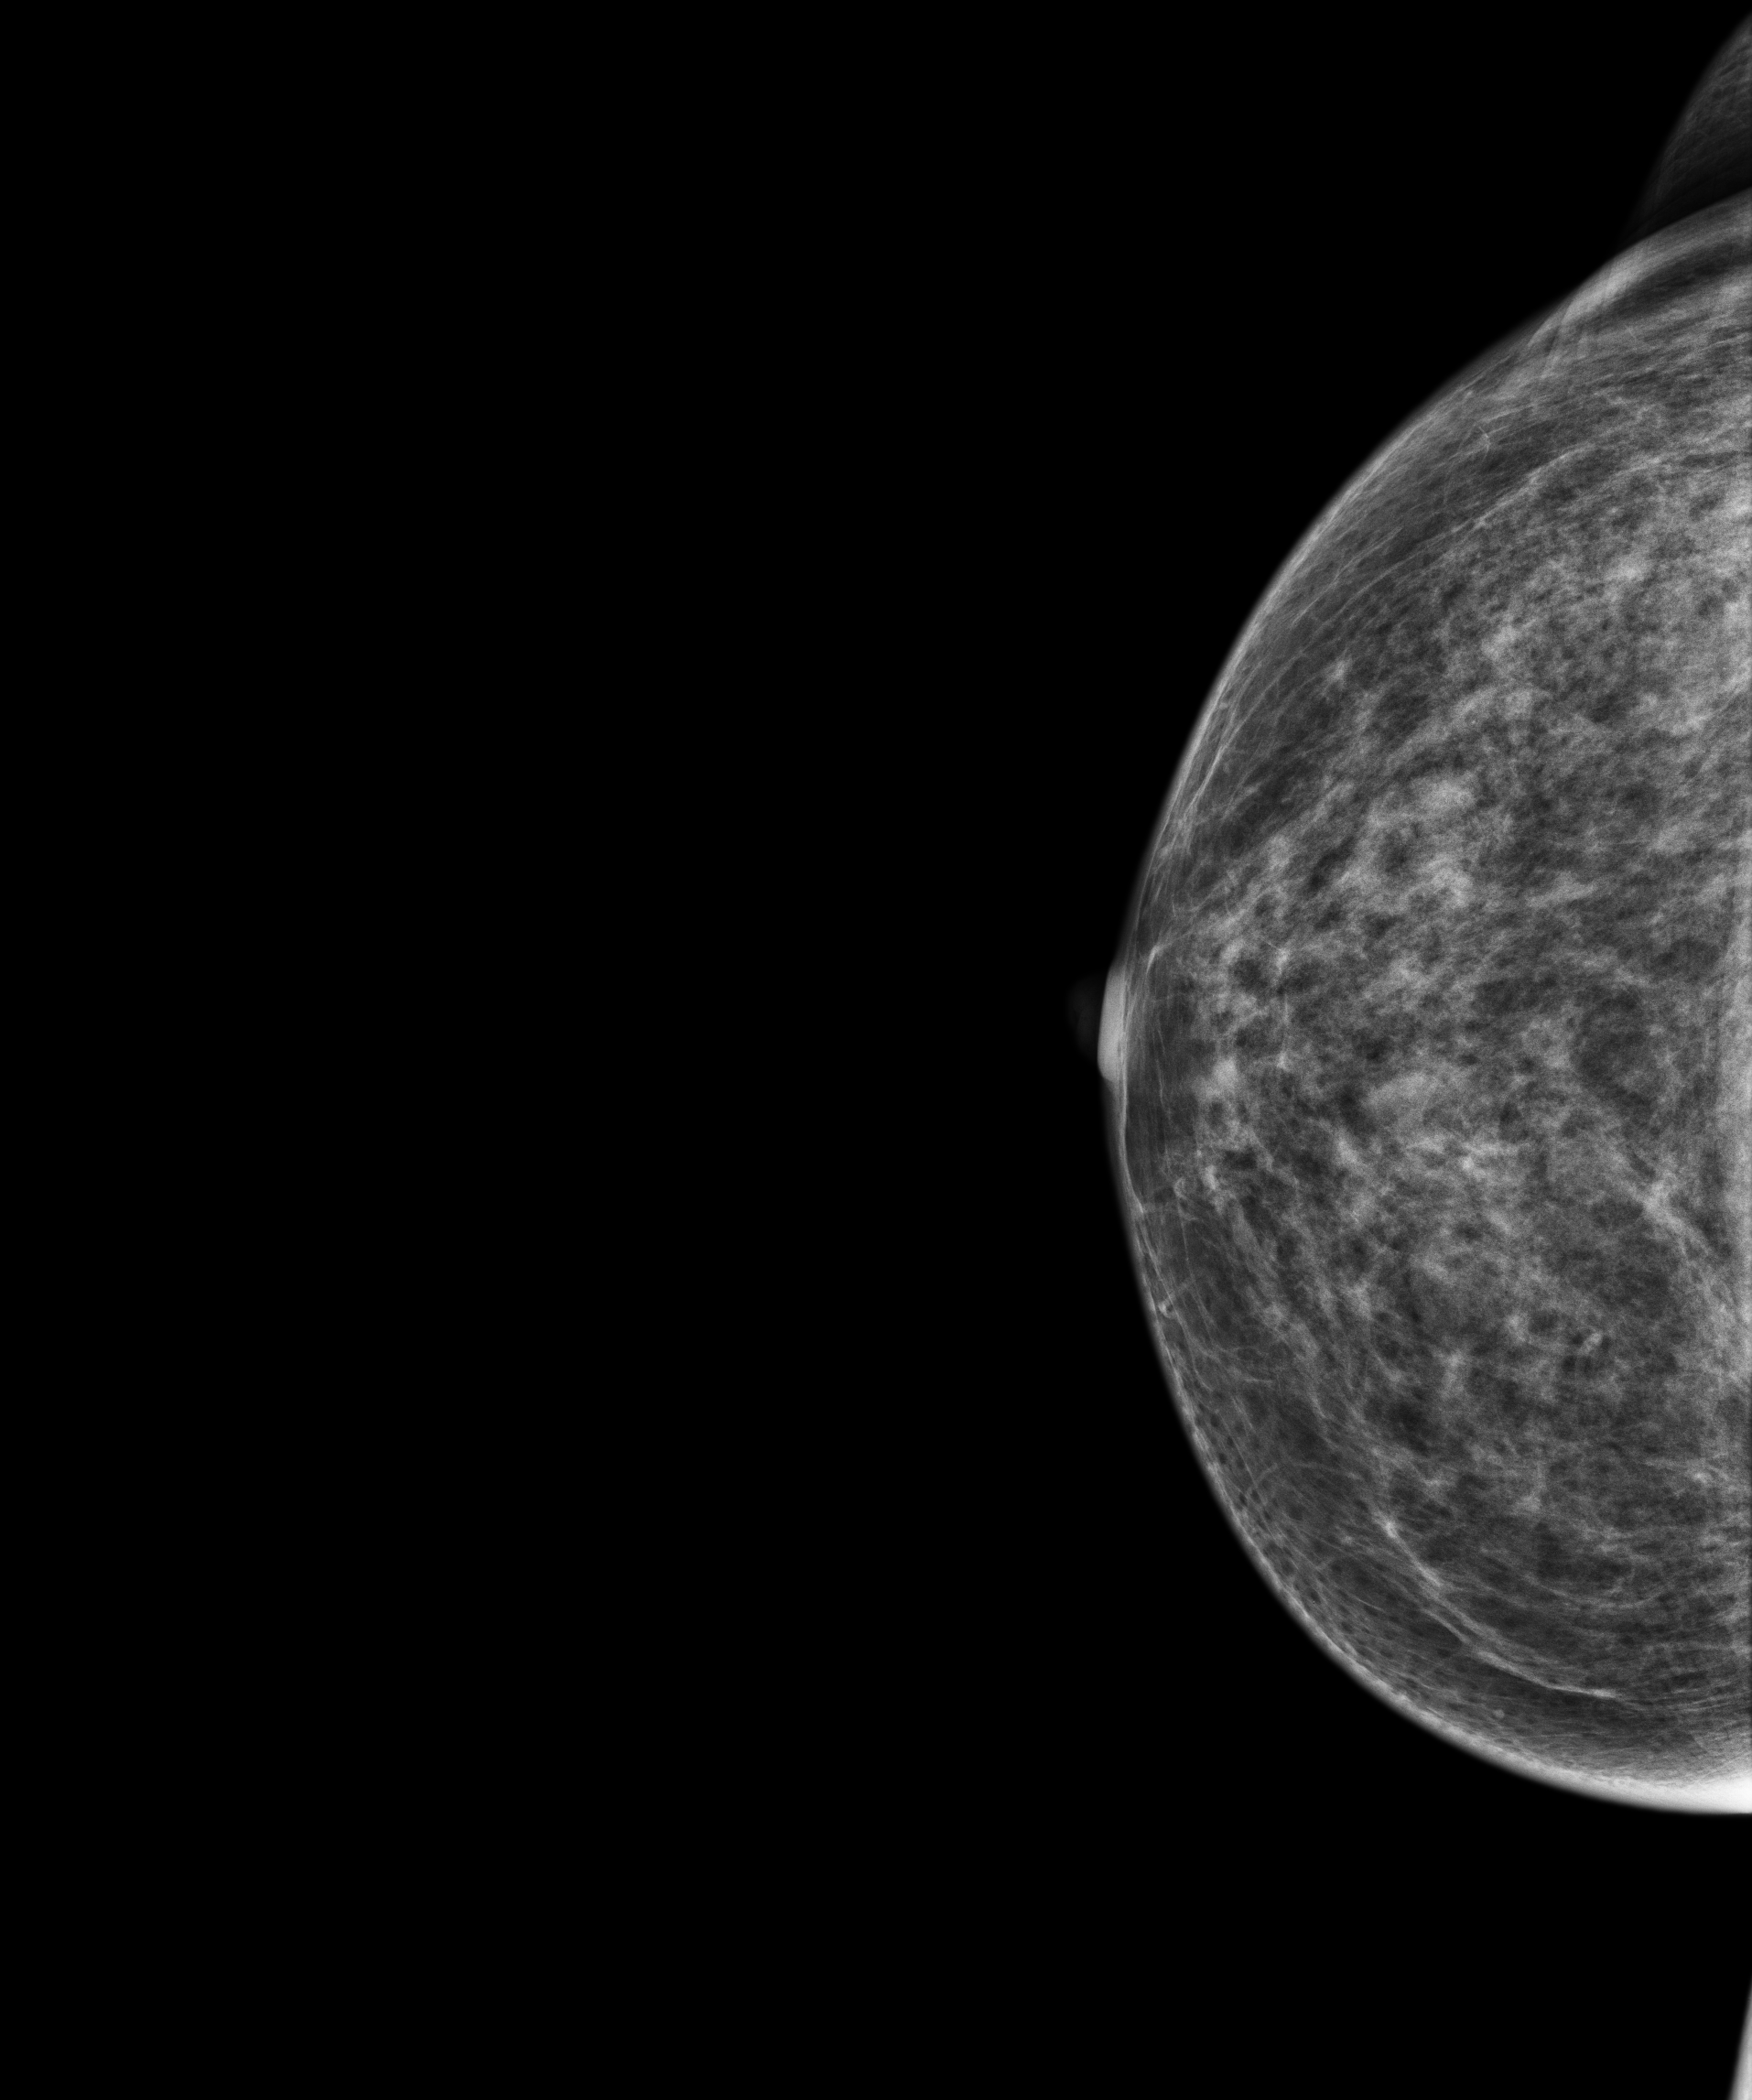
Digital mammogram (FFDM); right breast; CC view; annual screening mammography examination; compressed breast thickness 52 mm. Female patient, age 69 years.
BI-RADS breast density category at the screening exam (both breasts, scale 1–4): 3. Final BI-RADS category for the screening round (tomosynthesis exam, both breasts): category 1. Recall: no recall after this screen.